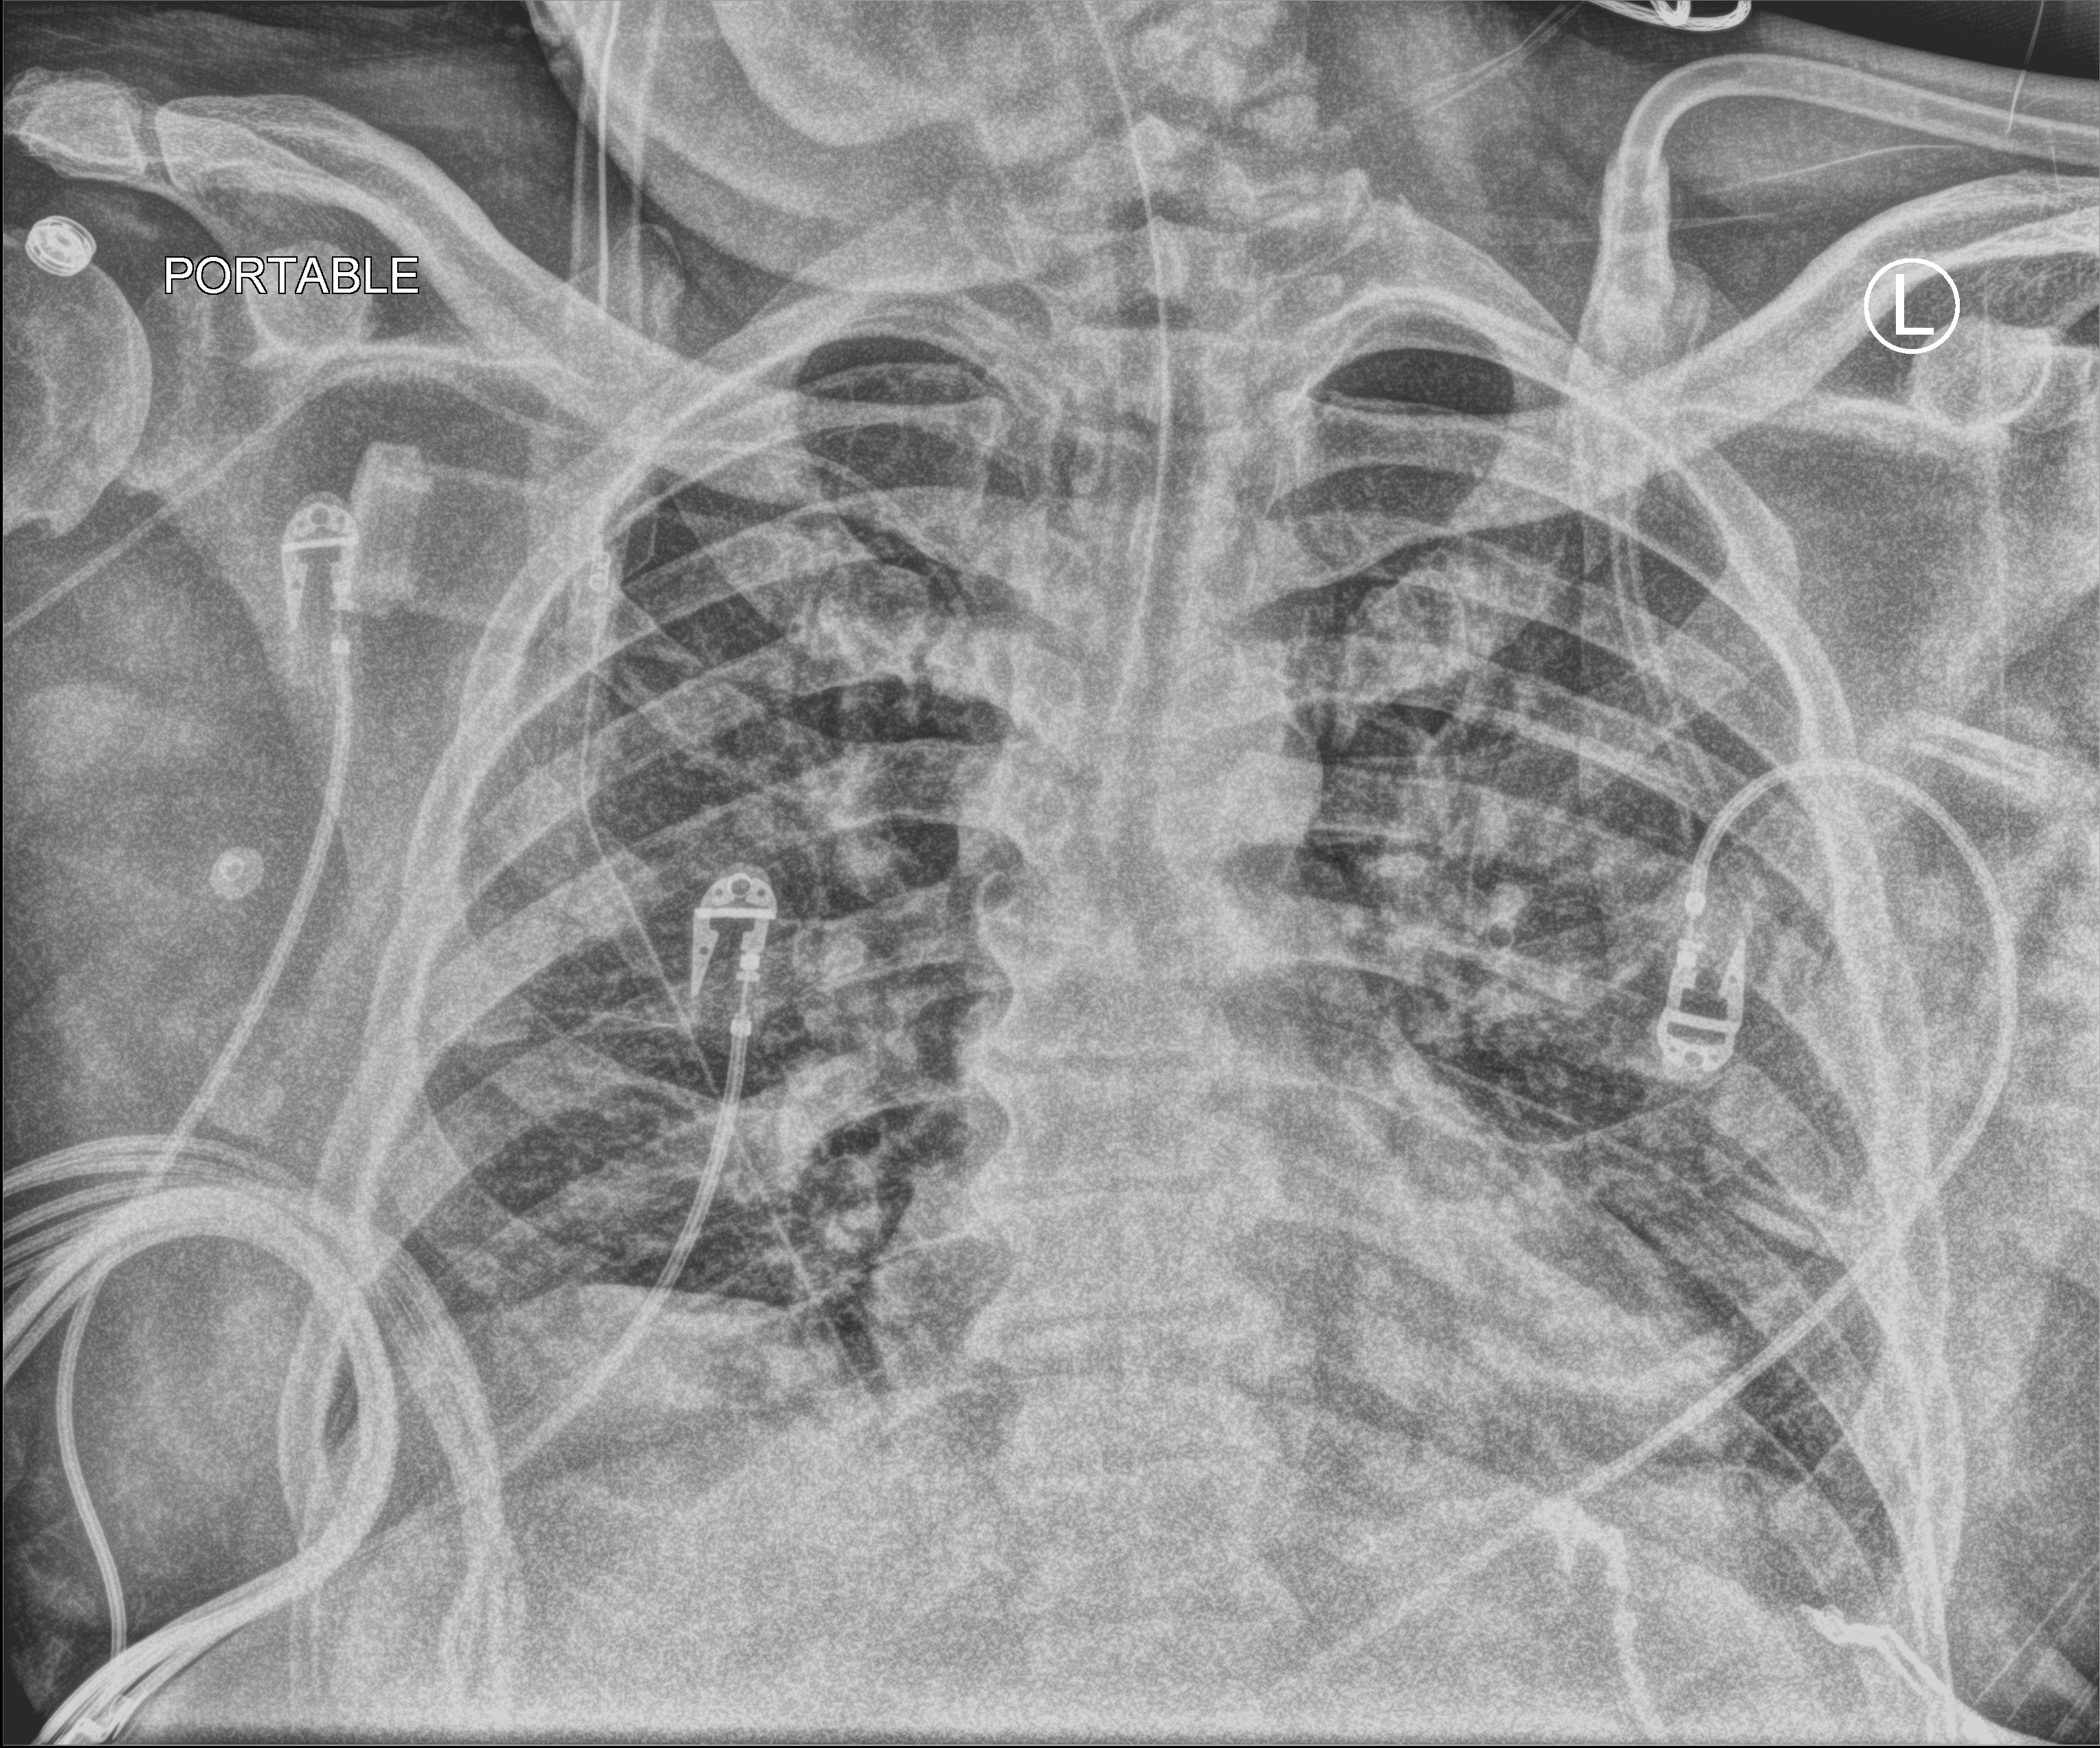
Portable chest radiograph; anteroposterior (AP) projection. Male patient hospitalised with COVID-19, age 18–59 years.
Hospital-stay facts (about this admission, not read from this image; timing relative to this image not recorded): admitted to intensive care during this hospital stay: yes; mechanically ventilated during this hospital stay: yes.